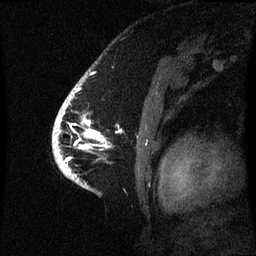
Breast MRI (dynamic contrast-enhanced), one sagittal slice. Slice 49 of 60 in the series (ordered by position). Dynamic contrast-enhanced series, image 2 of 3 at this slice position (ordered by acquisition). 1.5 T. TE 4.2 ms, TR 8.4 ms. 2.1 mm slice thickness. 256 × 256 image matrix. Female patient, age 53 years. From the clinical record (not read from this slice): setting: breast cancer imaged before/during neoadjuvant chemotherapy; receptor status: HR-positive, HER2-negative.
Outlined on this slice (semi-automatically segmented with operator editing):
- analysis volume of interest (the breast-tissue region the enhancement analysis was run in; not a lesion): box from (x=54, y=90) to (x=105, y=171) px
- tumour enhancement mask (voxels above the 70 % enhancement threshold inside the analysis volume of interest): (x=56, y=104)–(x=102, y=169)